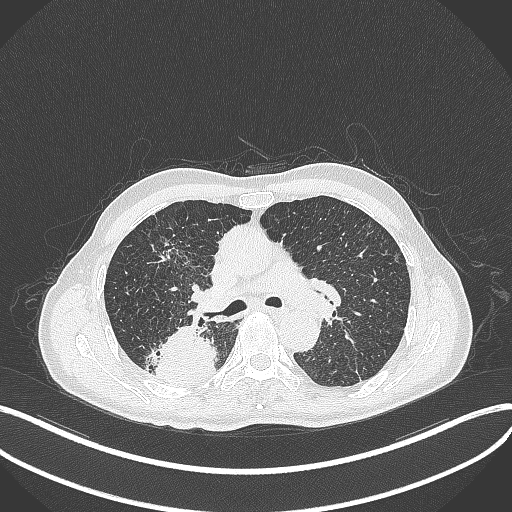
Chest CT, one axial slice. Slice 288 of 428 in the series (ordered by position). Reconstruction kernel B70f. 120 kVp. Lung window (W 1500 / L -600 HU). 1 mm slice thickness. 512 × 512 image matrix, field of view 400 × 400 mm. Male patient, age 79 years. Case-level facts recorded for this patient, not image findings: clinical TNM (as recorded): T3 N0 M0.
Structures marked on this image (bounding box drawn by a radiologist):
- lung tumour (recorded histology: adenocarcinoma): bounding box [x1, y1, x2, y2] px = [154, 326, 216, 384]